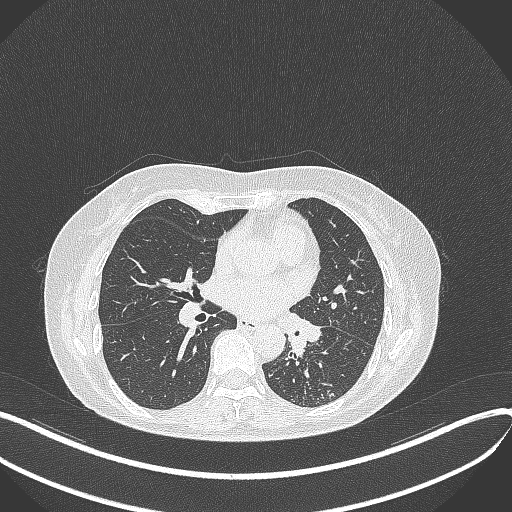
Chest CT, one axial slice; slice 205 of 429 in the series (ordered by position); 100 kVp; lung window (W 1500 / L -600 HU); 1 mm slice thickness; 512 × 512 image matrix. Female patient, age 63 years. From the clinical record (not read from this slice): clinical TNM (as recorded): T1b N0 M0.
Structures marked on this image (bounding box drawn by a radiologist):
- lung tumour (recorded histology: adenocarcinoma): bounding box <281,309,327,360> (left, top, right, bottom; pixels)